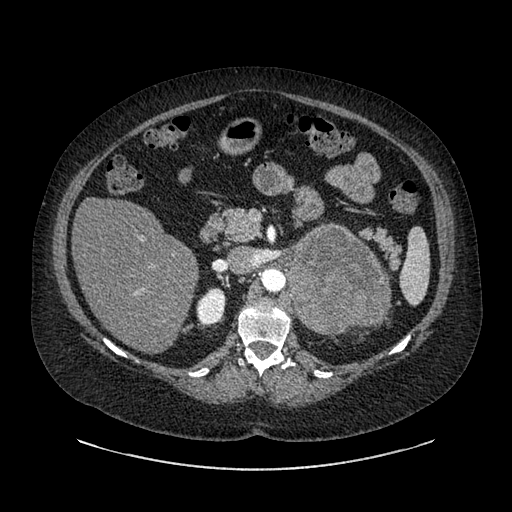
Contrast-enhanced abdominal CT, one axial slice. Position 550 of 769 along the scan axis. Intravenous contrast given. Soft-tissue window (W 400 / L 40 HU). 0.62 mm slice thickness. 512 × 512 image matrix. Patient: female, 61 years. Case-level facts recorded for this patient, not image findings: diagnosis: adrenocortical carcinoma; tumour side: left adrenal; tumour size at pathology: 13 cm.
Outlined on this slice (semi-automatically segmented with operator editing):
- mass: box from (x=289, y=226) to (x=387, y=334) px